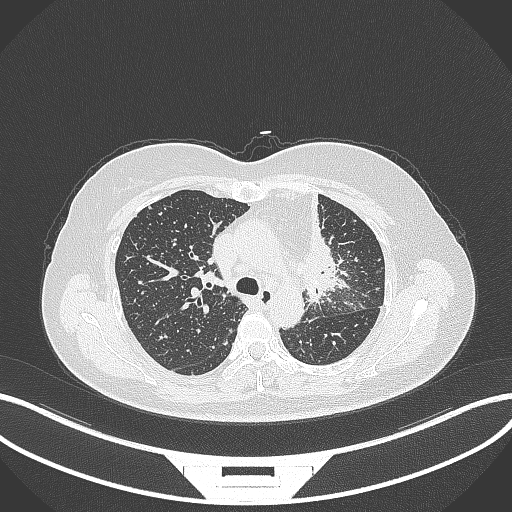
Chest CT, one axial slice. Slice 228 of 348 in the series (ordered by position). Reconstruction kernel B70f. Lung window (W 1500 / L -600 HU). 1 mm slice thickness. 512 × 512 image matrix. Female patient, age 49 years. Case-level facts recorded for this patient, not image findings: clinical TNM (as recorded): T1c N0 M1.
Structures marked on this image (bounding box drawn by a radiologist):
- lung tumour (recorded histology: adenocarcinoma): bounding box [x1, y1, x2, y2] px = [292, 185, 352, 304]